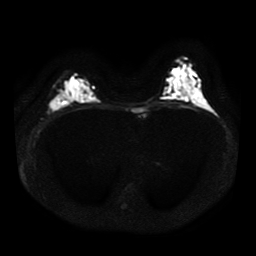
Breast MRI, one axial slice; slice 24 of 41 in the series (ordered by position); diffusion-weighted series; image 2 of 4 stored at this slice position (different b-values; order by instance number); 1.5 T; 5 mm slice thickness; 256 × 256 image matrix. Female patient.
Structures marked on this image (manually delineated by an expert):
- tumour on diffusion-weighted imaging: box from (x=50, y=102) to (x=59, y=110) px